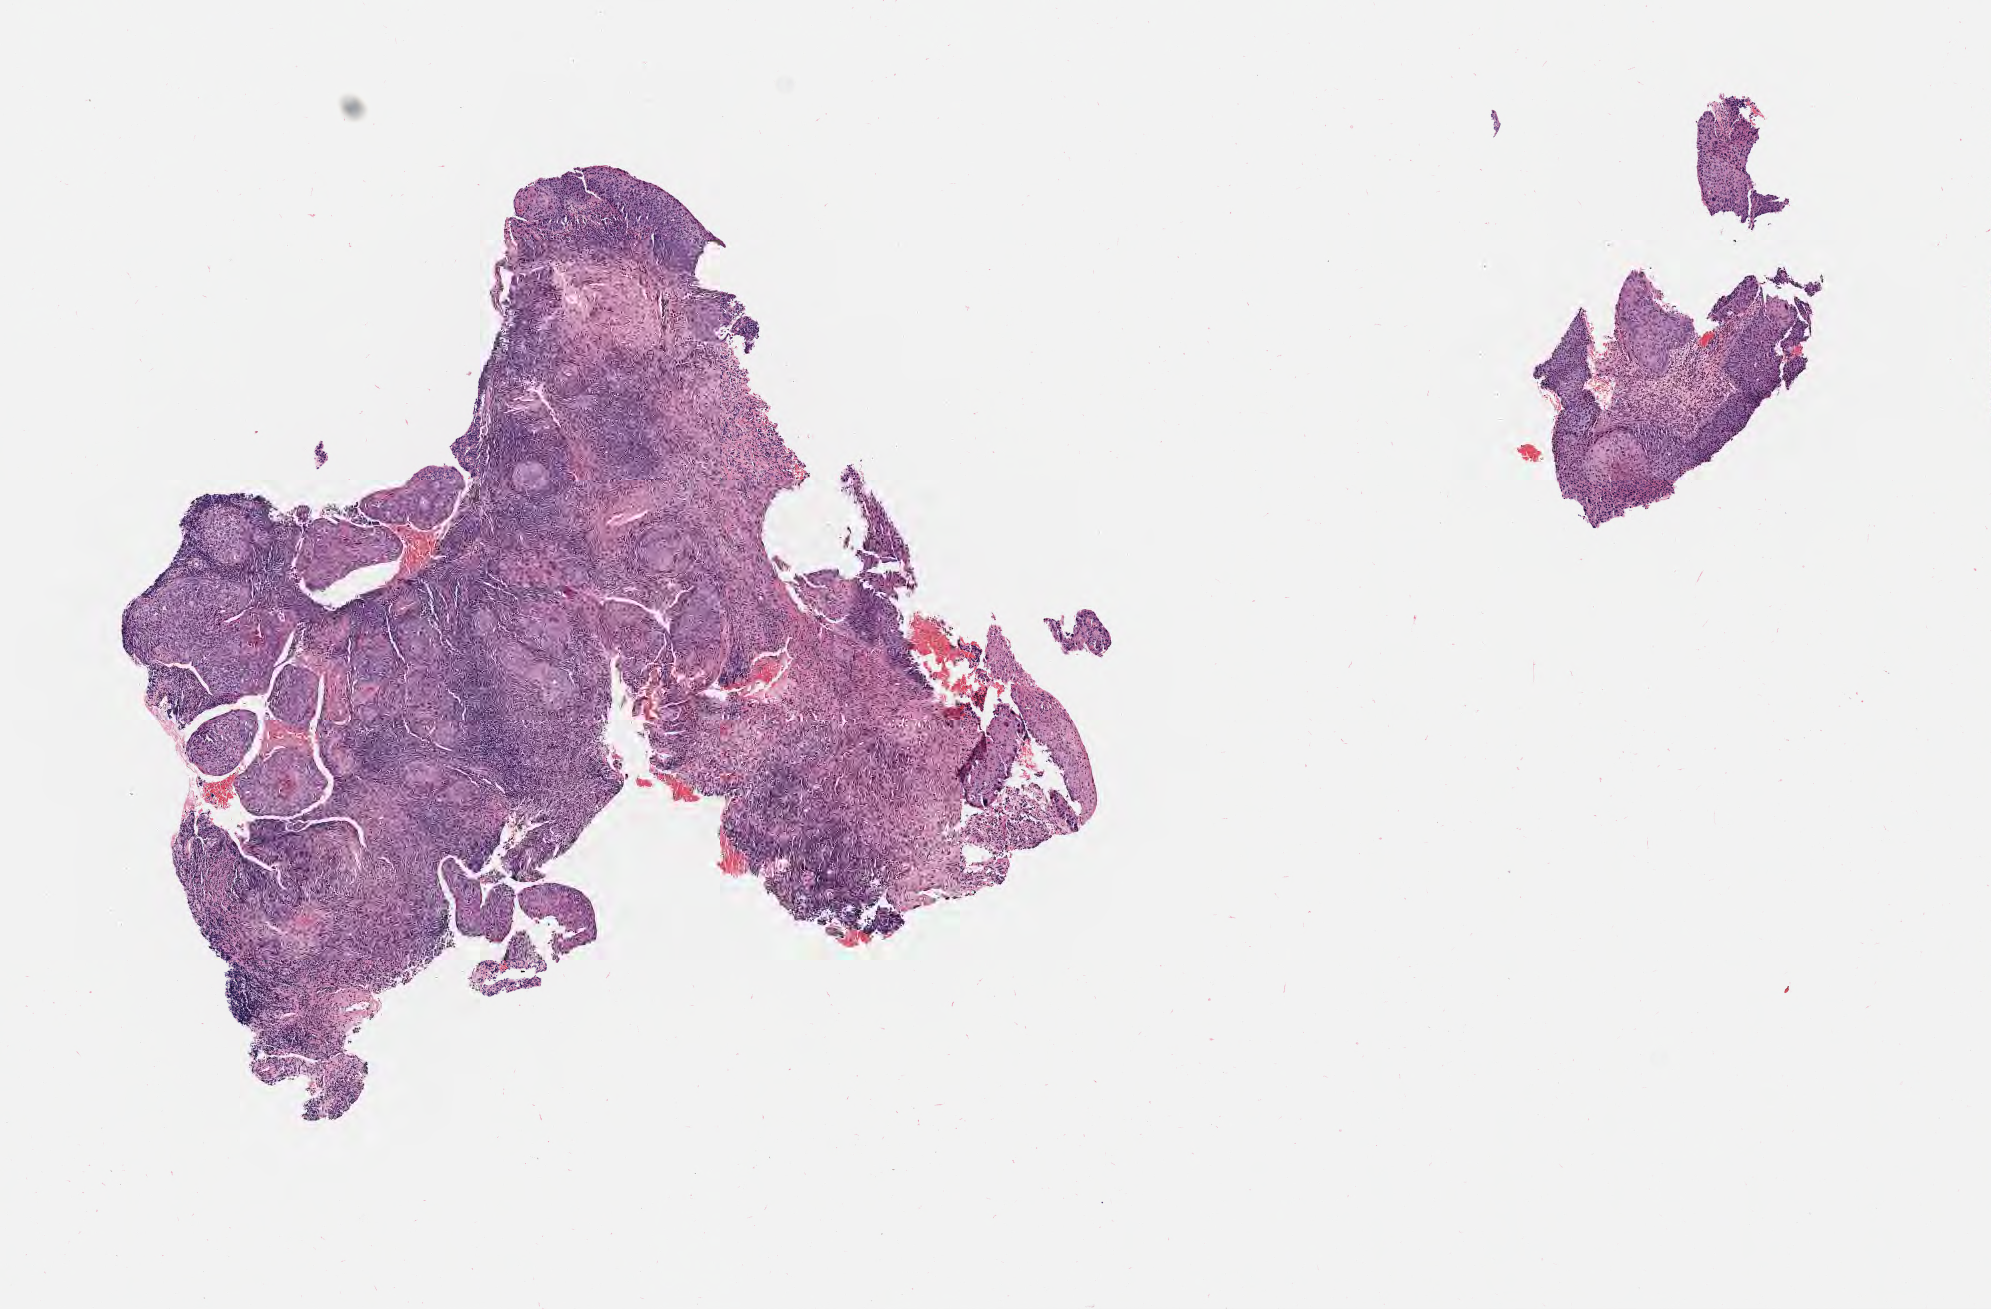
Digitized hematoxylin and eosin (H&E)-stained section, shown as a low-resolution overview of the whole scanned area (about 8.1 x 5.3 mm), specimen: tumor tissue, site: cervix. Female patient, 40 years old.
Histologic diagnosis: Squamous cell carcinoma, keratinizing, NOS.